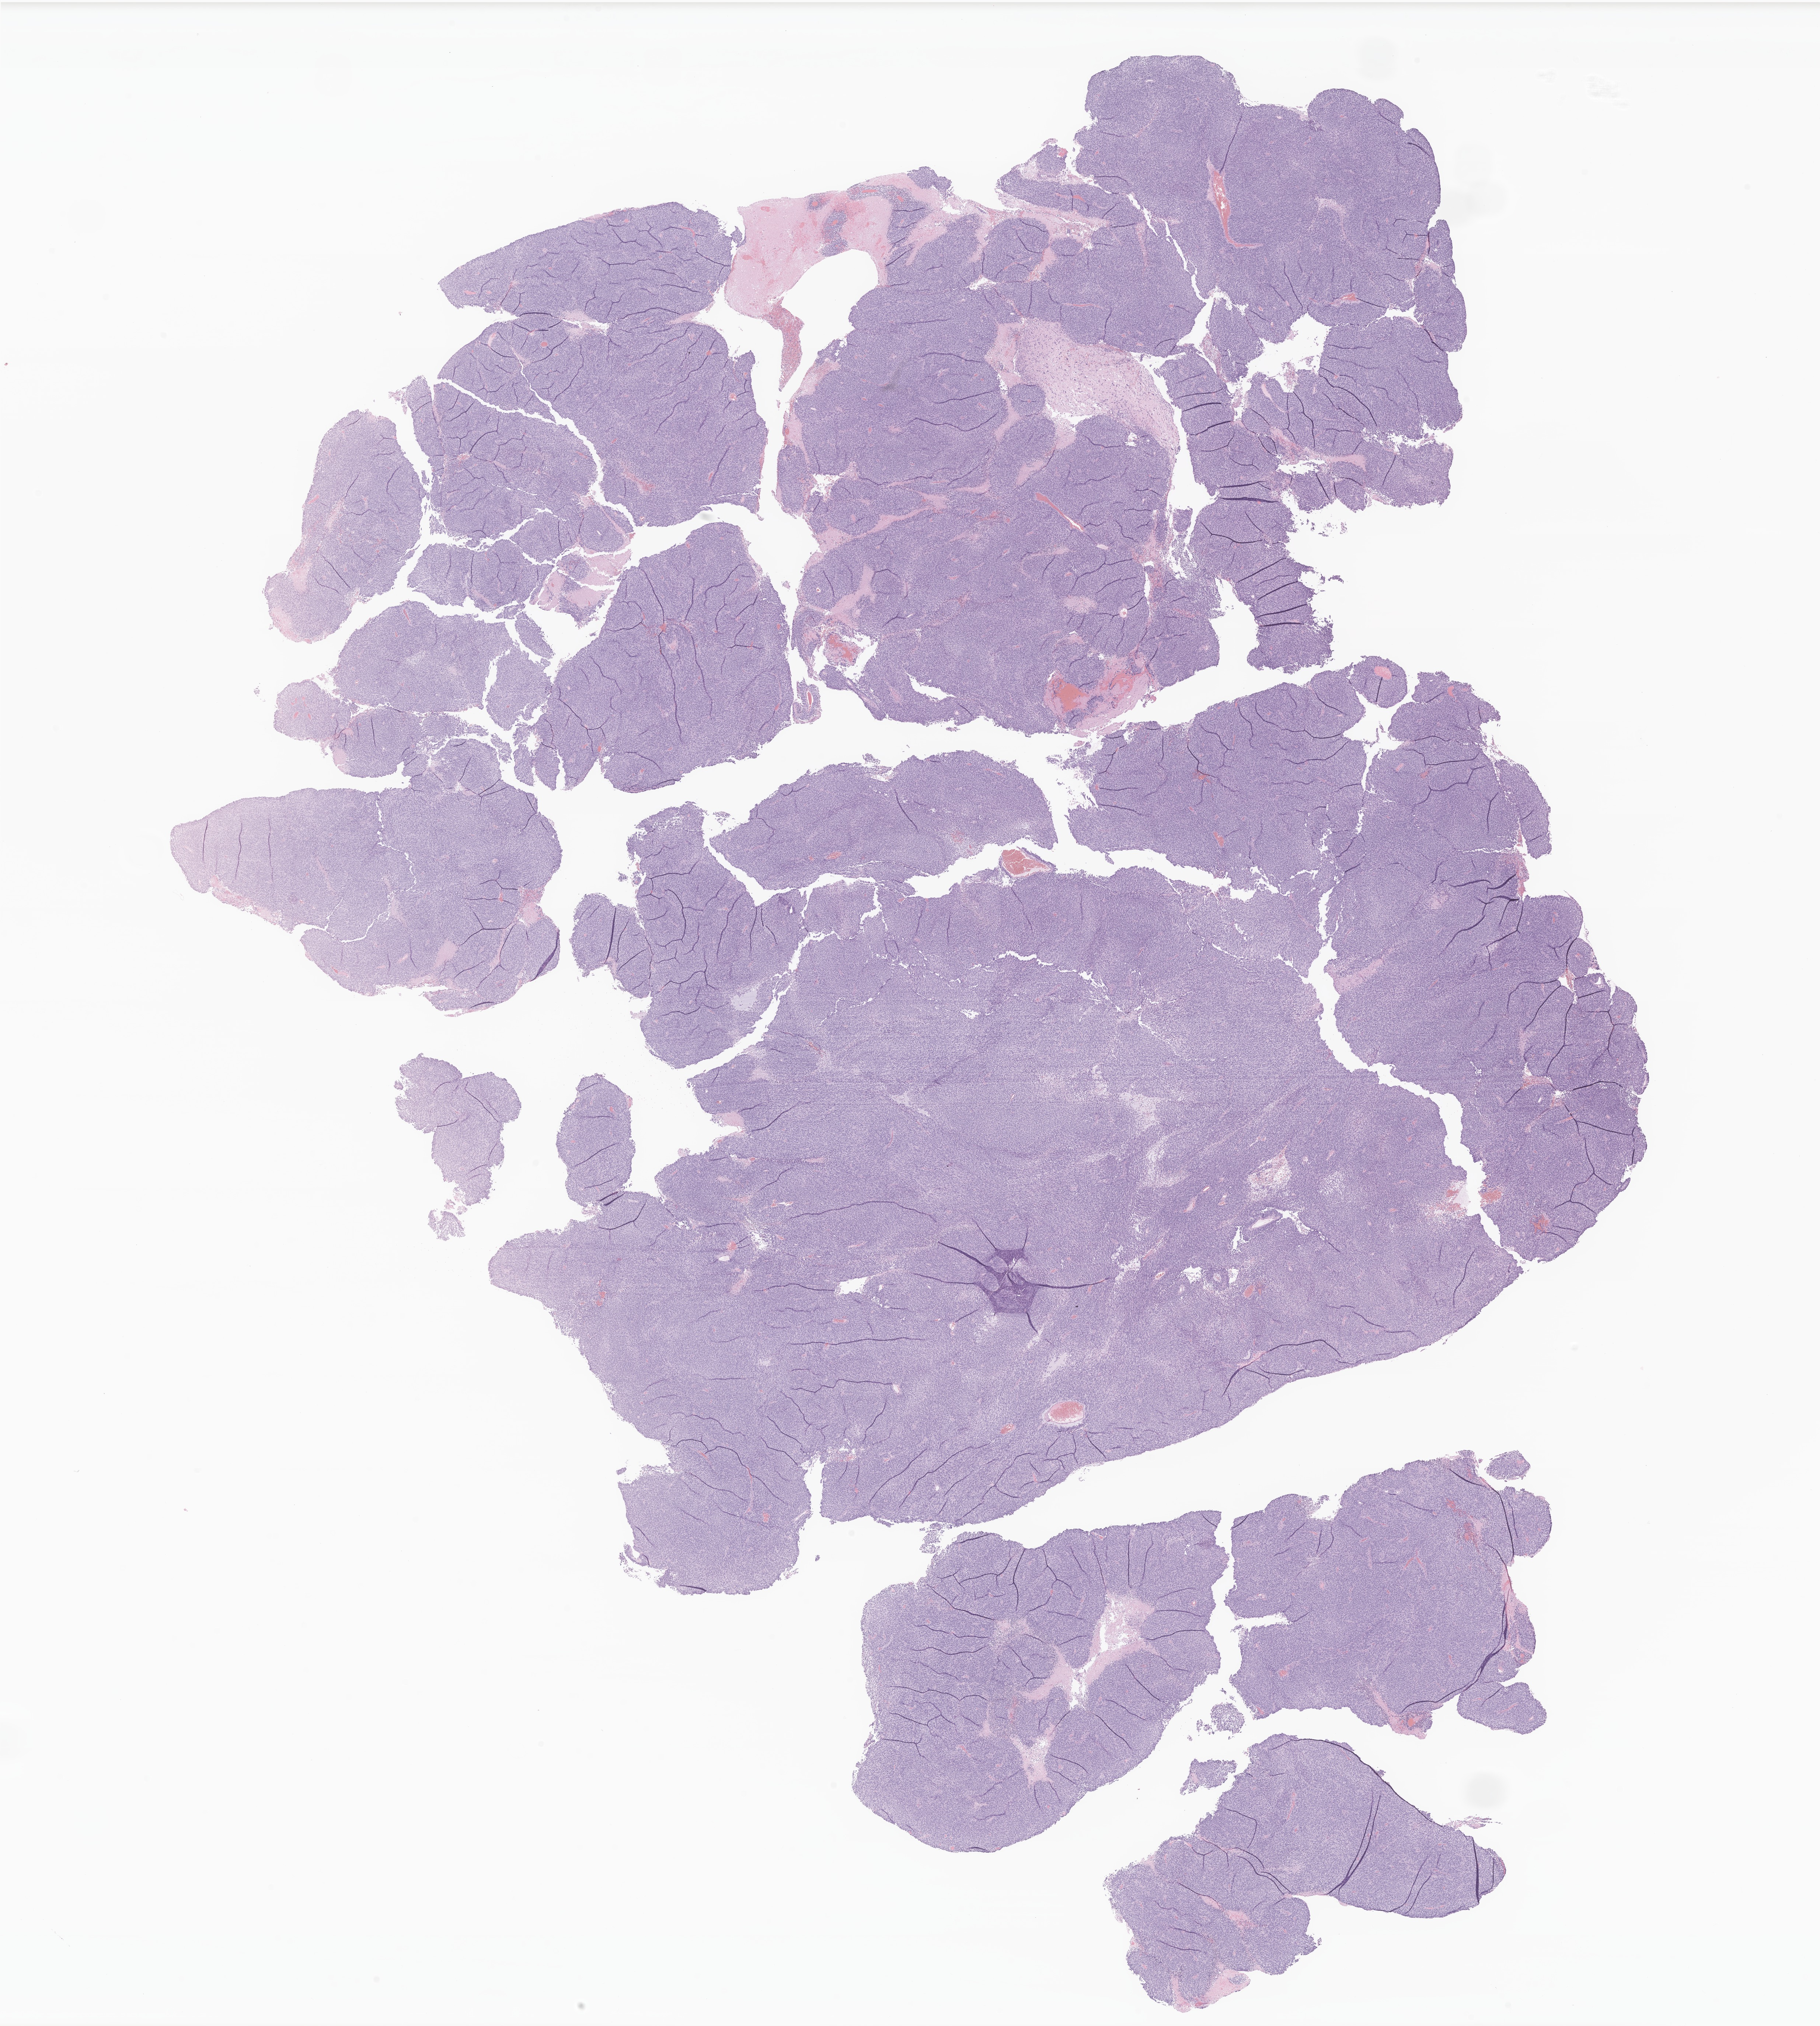
H&E whole-slide image of tumor tissue from the parietal lobe — whole scanned area (about 20.8 x 23.2 mm) shown as a low-resolution overview. Formalin-fixed paraffin-embedded section. Patient female; age 121 months.
Diagnosis (ICD-O-3 morphology term): Glioma, malignant.